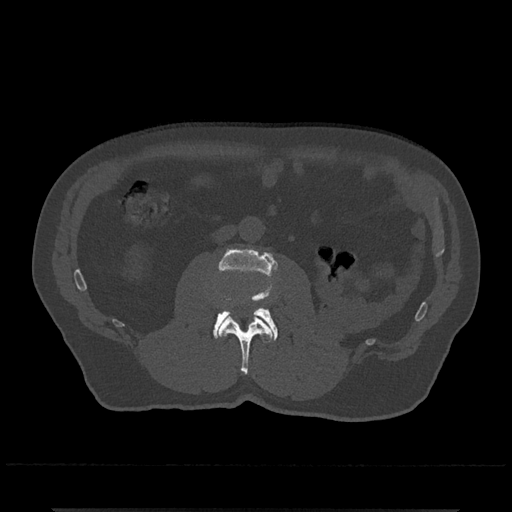
CT including the spine, one axial slice; slice 260 of 797 in the series (ordered by position); reconstruction kernel Br40s/3; 120 kVp; bone window (W 1800 / L 400 HU); 0.5 mm slice thickness; 512 × 512 image matrix. Patient: male, 67 years. Case-level facts recorded for this patient, not image findings: primary cancer: prostate.
Structures marked on this image (semi-automatic segmentation, software-assisted and operator-edited):
- L2 vertebra: bounding box <219,314,273,374> (left, top, right, bottom; pixels)
- L3 vertebra: <213,248,278,341>